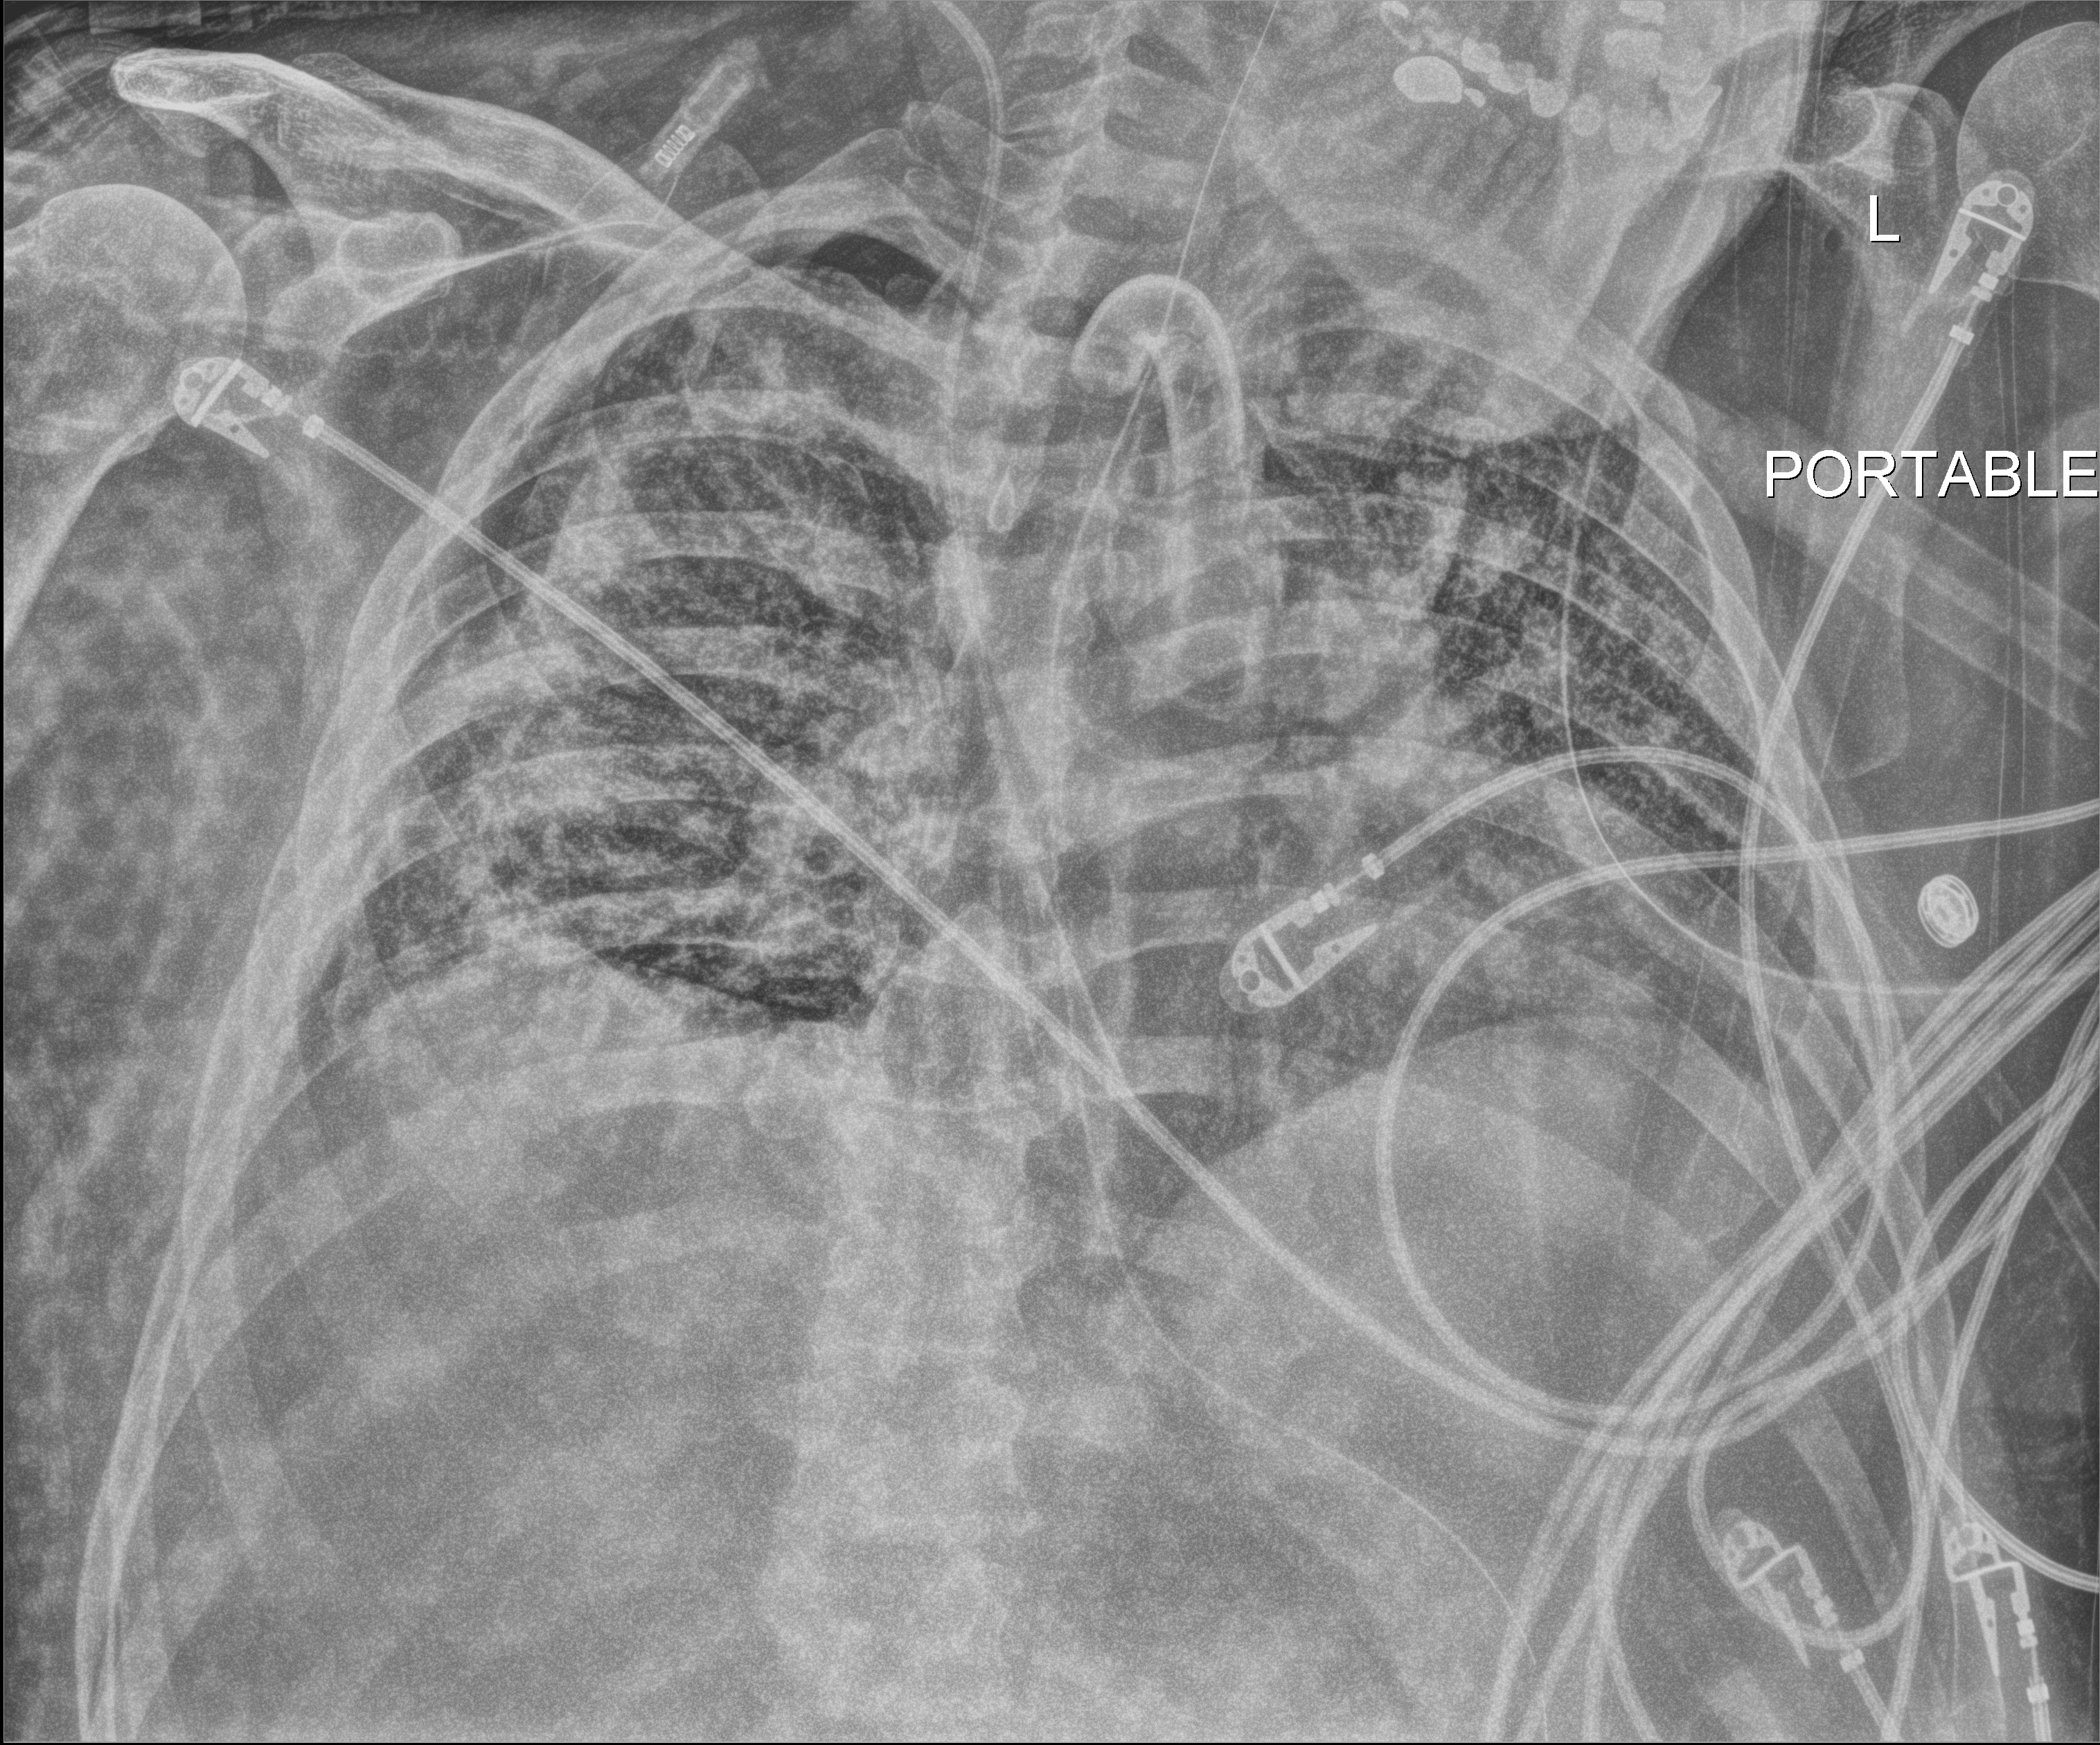
Portable chest radiograph. Male patient hospitalised with COVID-19, age 18–59 years.
Admission-level facts for this patient (not findings on this image; timing relative to this image not recorded): mechanically ventilated during this hospital stay: yes.